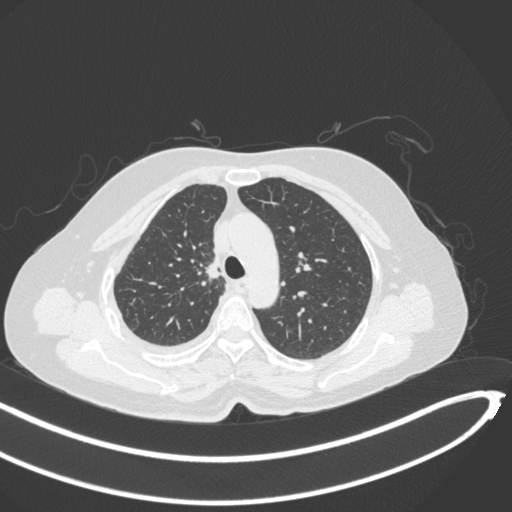
Chest CT, one axial slice; position 225 of 297 along the scan axis; 120 kVp; lung window (W 1500 / L -600 HU); 512 × 512 image matrix, field of view 400 × 400 mm. Patient: female, 64 years. From the clinical record (not read from this slice): clinical TNM (as recorded): T1b N0 M1.
Annotated regions visible in this slice (bounding box drawn by a radiologist):
- lung tumour (recorded histology: adenocarcinoma): bounding box (x1, y1, x2, y2) in pixels: (201, 252, 224, 284)